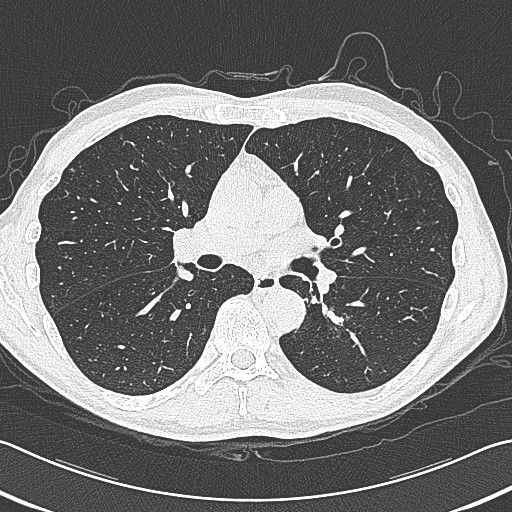
Chest CT (low-dose screening protocol), one axial image; baseline screening round; lung window (W 1500 / L -600 HU); lung (sharp) reconstruction kernel (B80f); slice 159 of 354 in the series; 512 × 512 image matrix. Male participant, aged 59 years at enrolment.
- Expert reader's lesion annotation, bounding box <314,291,375,353> (left, top, right, bottom; pixels).
- The exam's reader record, not a measurement of the box and not confirmed to be the same lesion: non-calcified nodule or mass ≥4 mm, left lower lobe, 15 × 15 mm, smooth margins, soft tissue attenuation.
- Official screen result: positive, change unspecified: nodule(s) >= 4 mm or enlarging nodule(s), mass(es), or other non-specific abnormalities suspicious for lung cancer.
- Participant outcome: lung cancer diagnosed 17 days after this screen — squamous cell carcinoma, large cell, nonkeratinizing, NOS, left lower lobe, poorly differentiated (G3), stage IB (AJCC 6th edition), 31 mm at pathology.